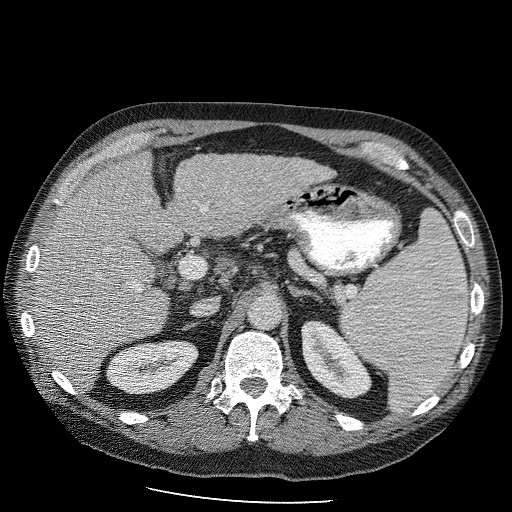
Contrast-enhanced abdominal CT (liver protocol), one axial slice. Slice 56 of 98 in the series (ordered by position). 120 kVp. Soft-tissue window (W 400 / L 40 HU). 2.5 mm slice thickness. 512 × 512 image matrix. From the clinical record (not read from this slice): diagnosis: hepatocellular carcinoma (patient treated with transarterial chemoembolisation; whether this scan precedes or follows treatment is not stated here); TNM stage (as recorded): Stage-II; Child-Pugh class: B; tumour differentiation: moderately differentiated; tumour nodularity: uninodular.
Structures marked on this image (semi-automatic segmentation, software-assisted and operator-edited):
- liver parenchyma outside the tumour (the mass and vessels are separate outlines, so this box may not span the whole liver): bounding box [x1, y1, x2, y2] px = [30, 152, 339, 390]
- liver vessels: [36, 202, 209, 291]